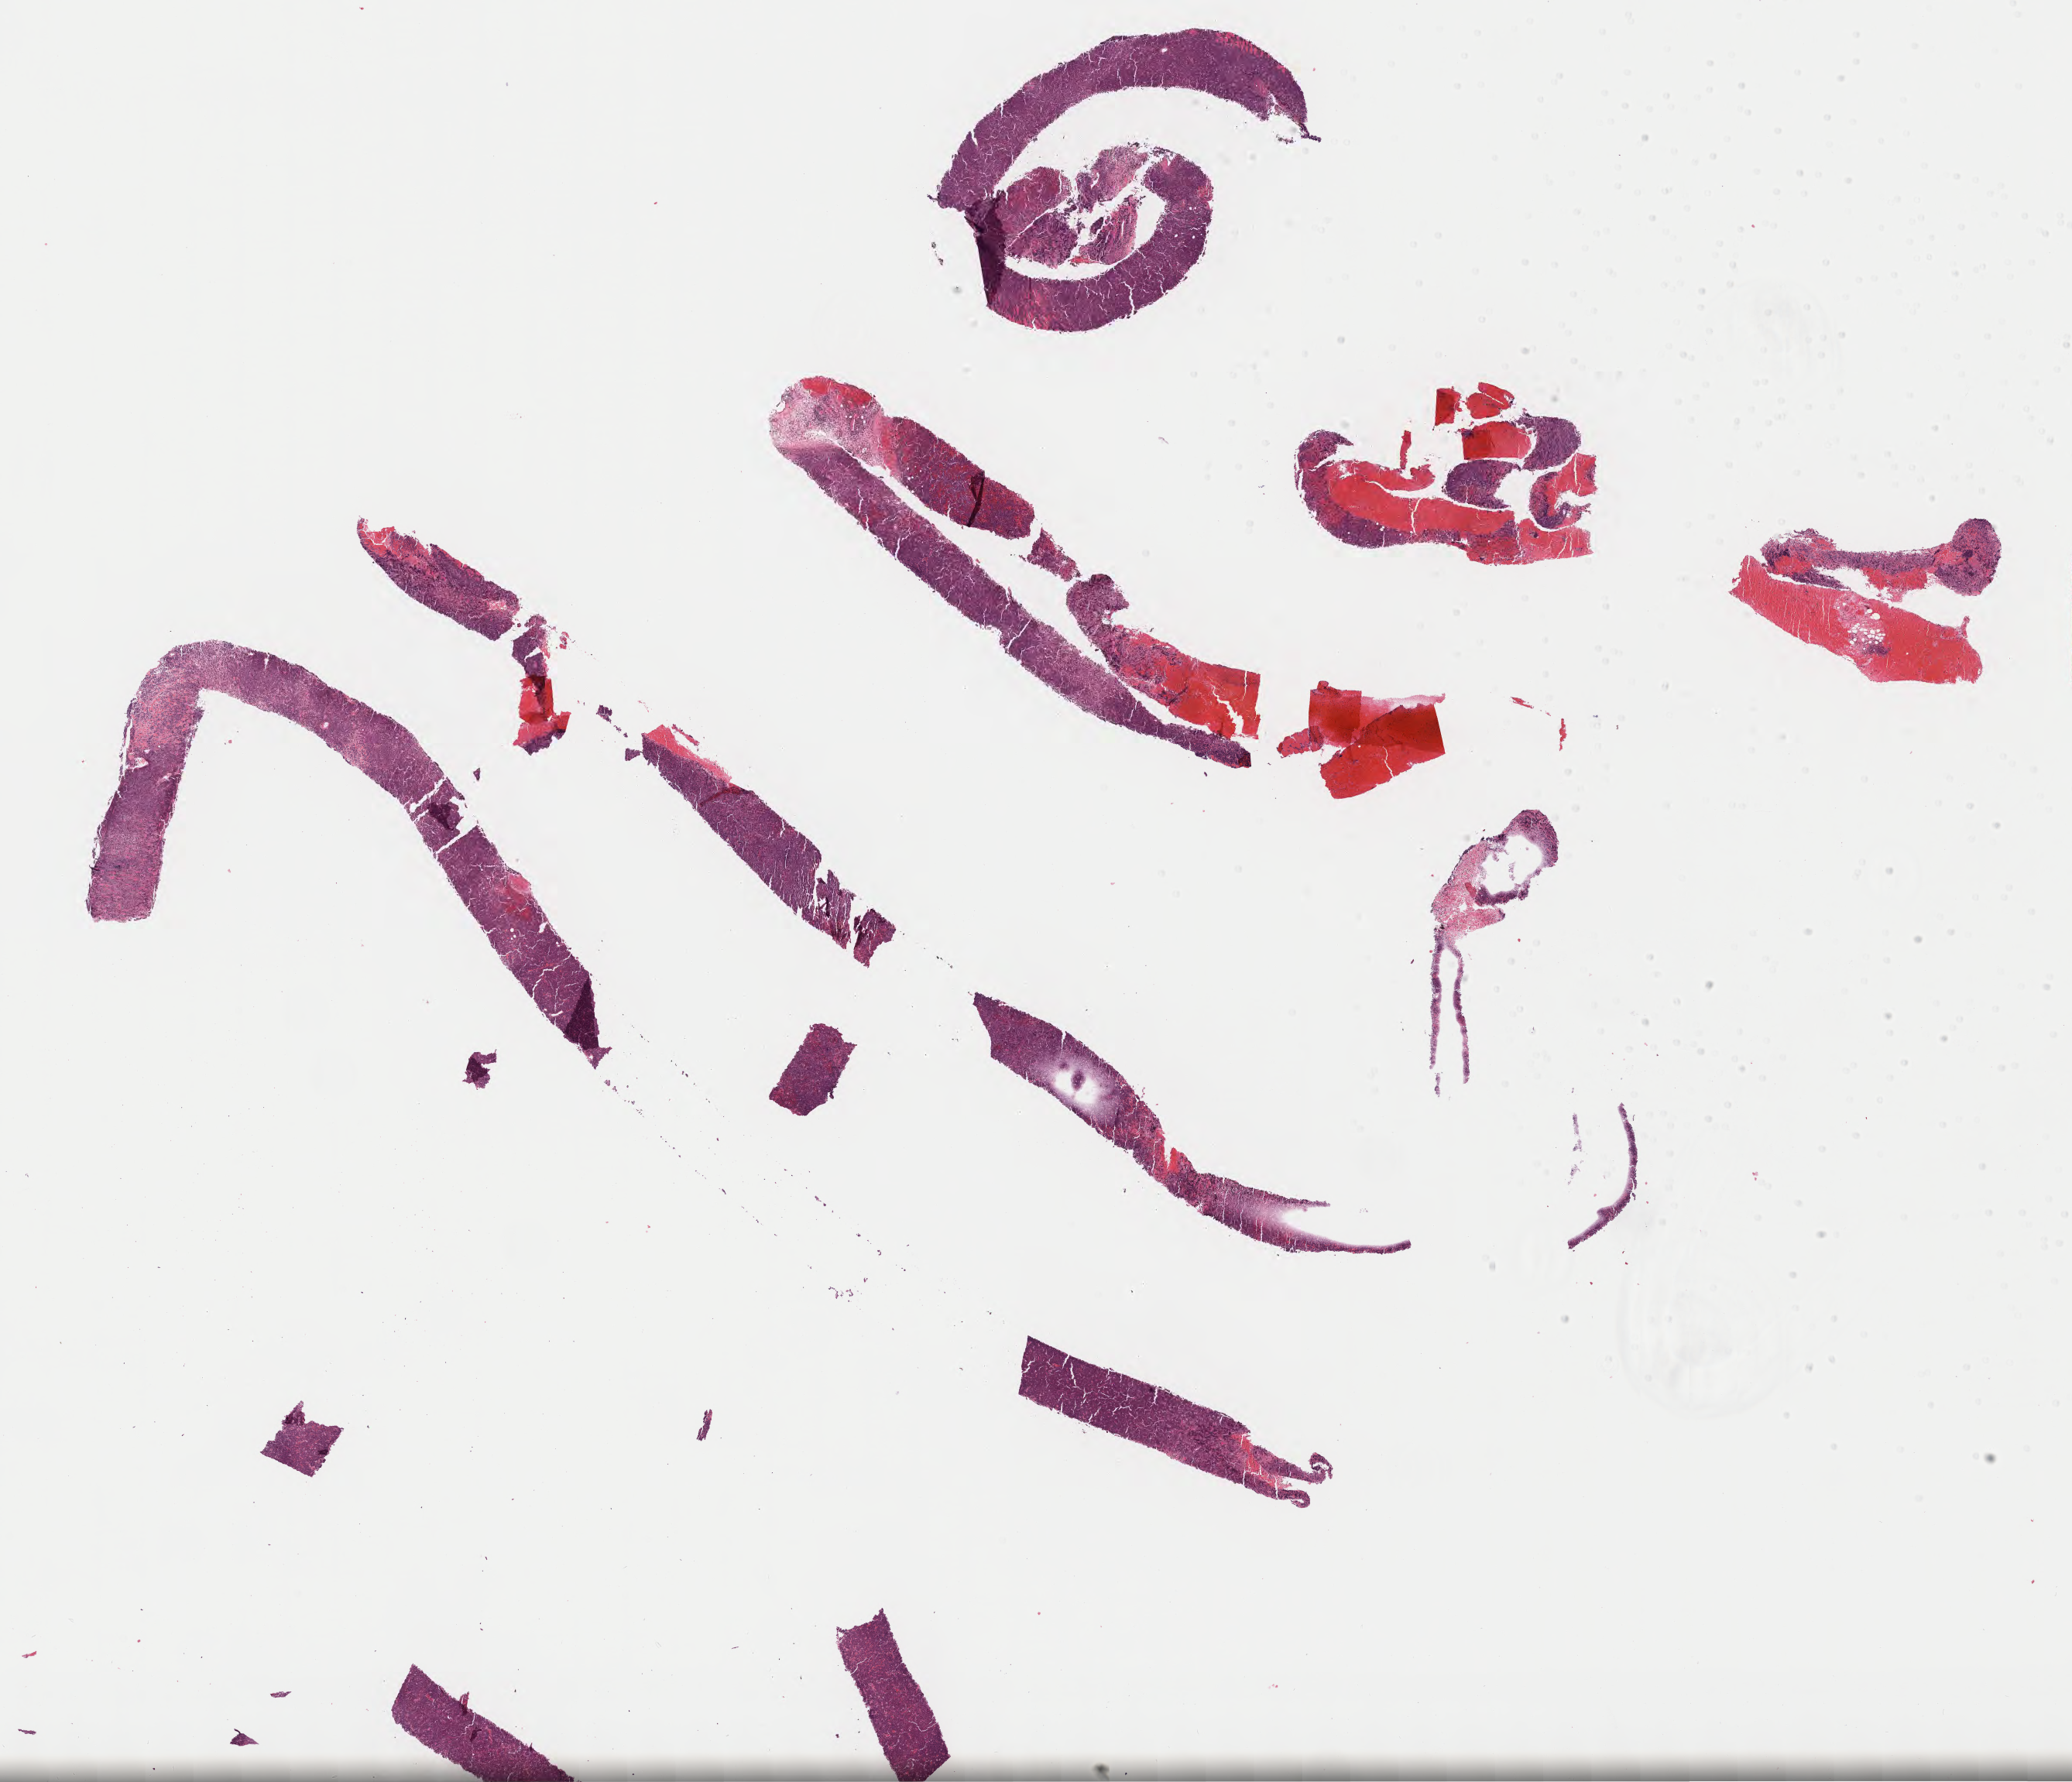
Whole-slide image, haematoxylin and eosin stain, low-resolution overview of the scanned area, about 21.6 x 18.6 mm, specimen: tumor tissue. Patient male; aged 45.
Diagnosis: Burkitt lymphoma, NOS.